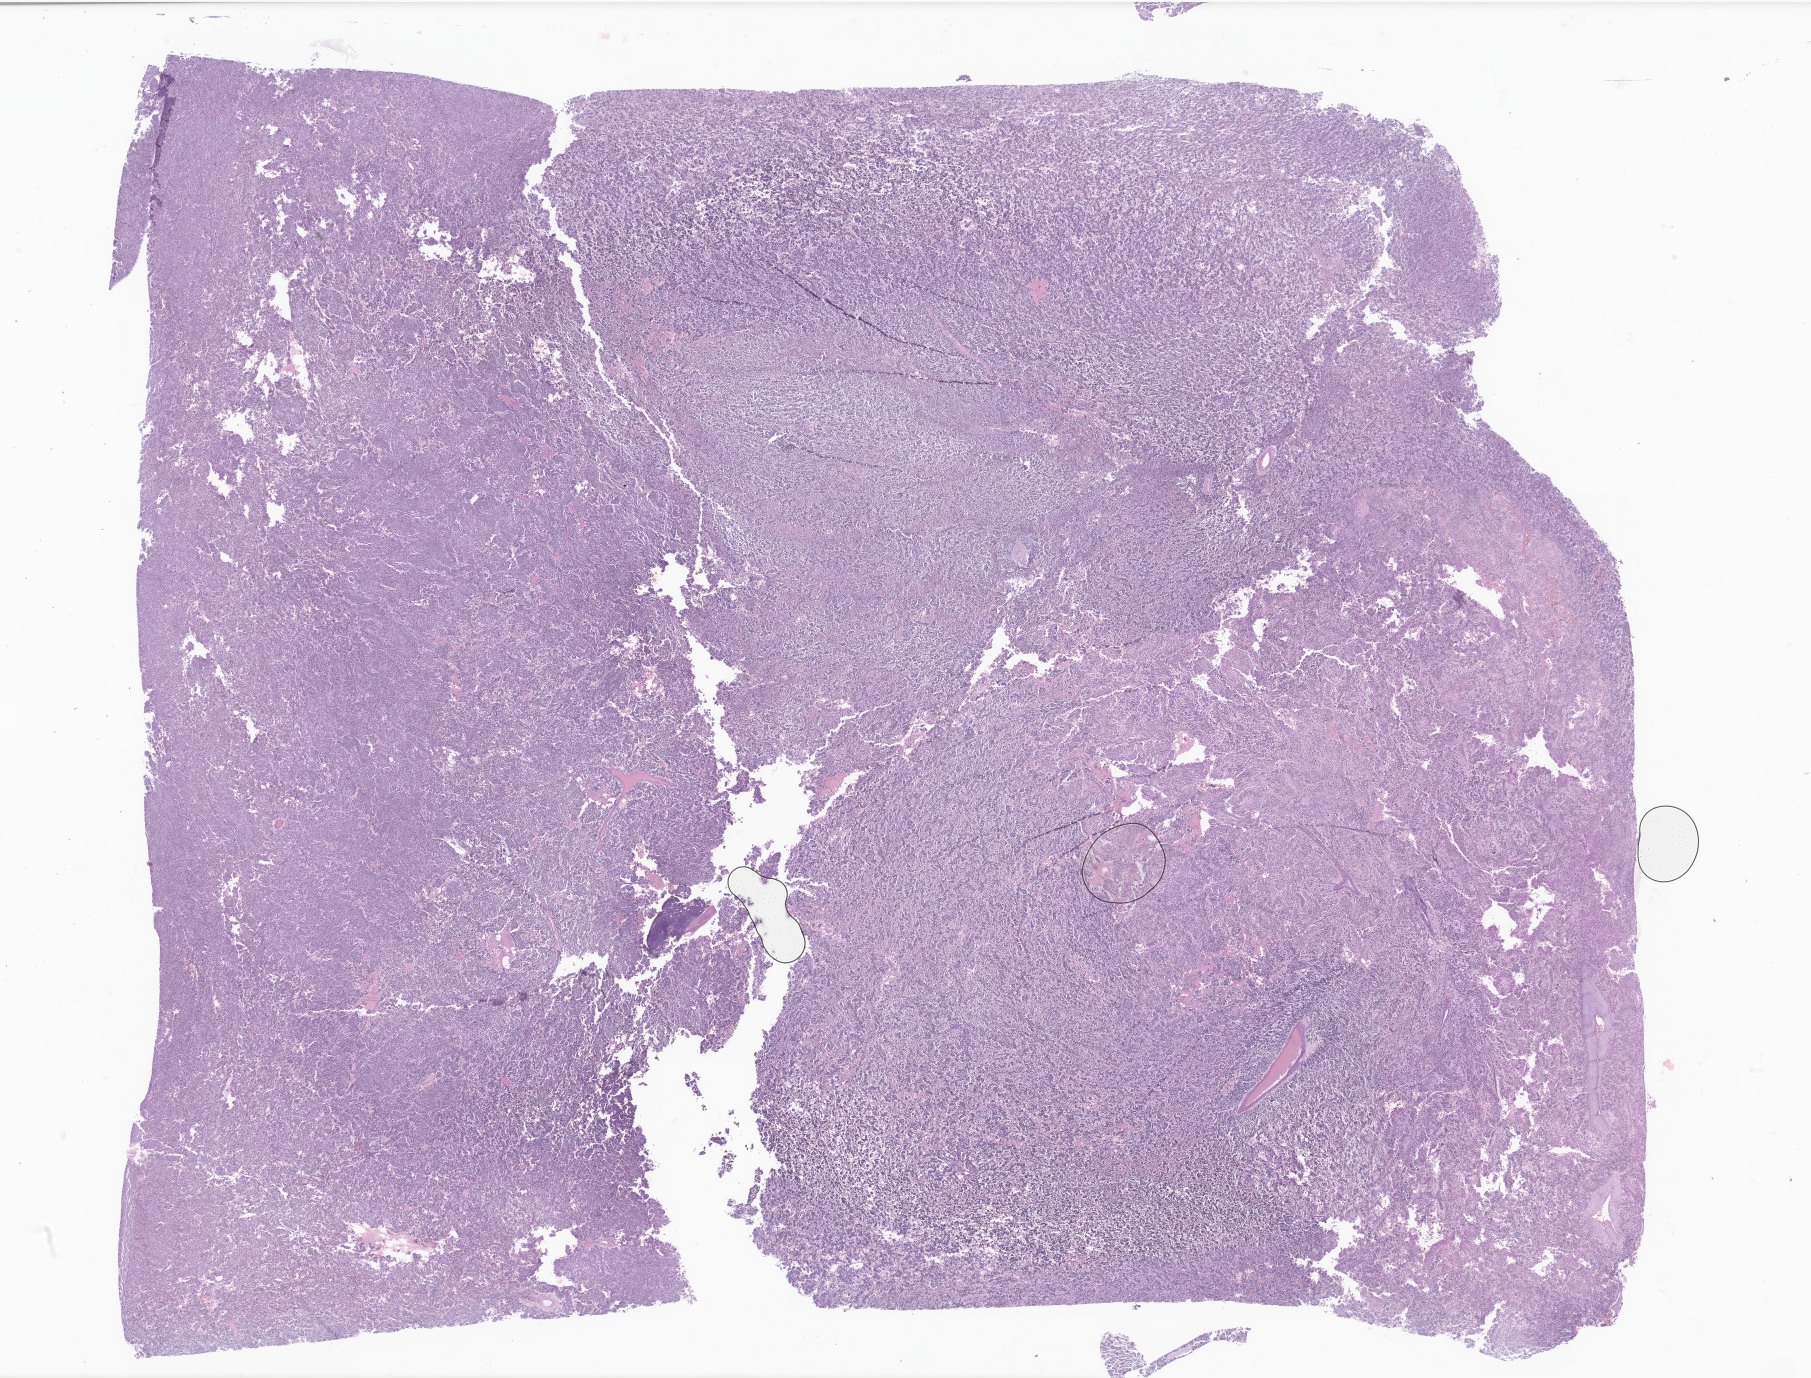
Whole-slide image, haematoxylin and eosin stain of tumor tissue from the abdomen — whole scanned area (about 30.5 x 23.2 mm) shown as a low-resolution overview. FFPE section. Patient female; age 807 days (about 2.2 years).
• diagnosis (ICD-O-3 morphology term): Neuroblastoma, NOS